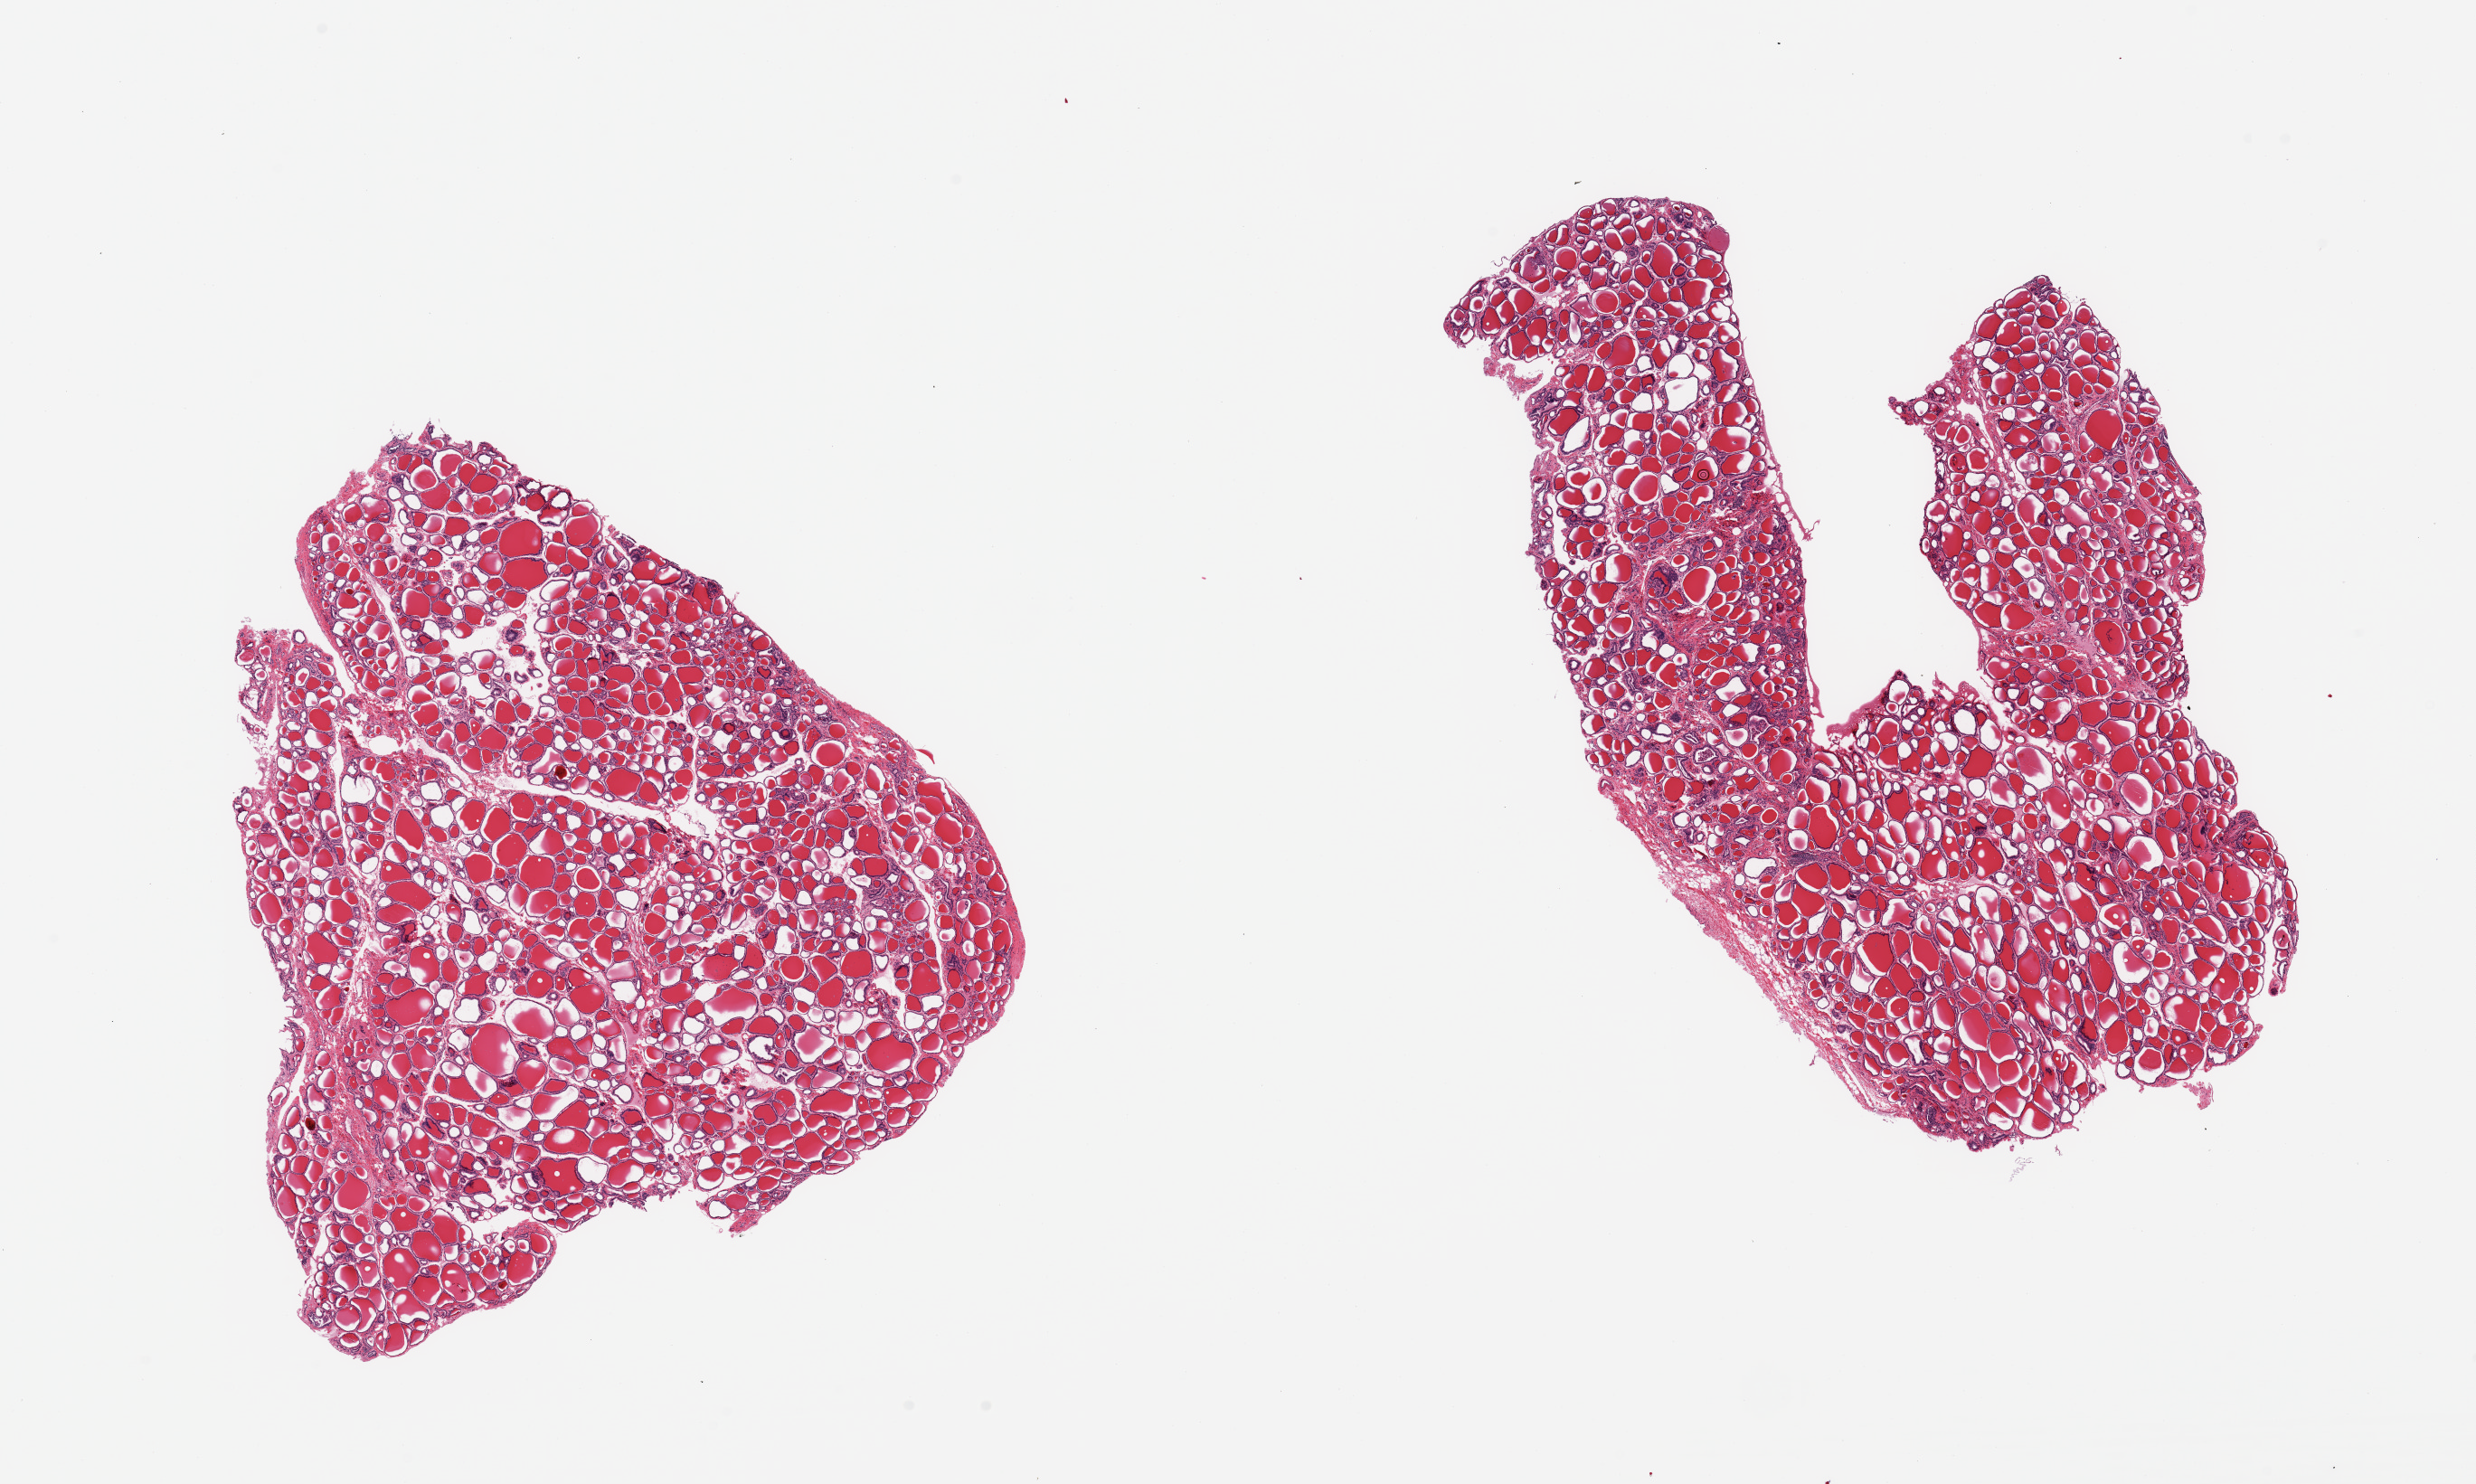
Hematoxylin and eosin (H&E) whole-slide image, low-resolution overview of the scanned area, about 21.7 x 13.0 mm (from a 20x scan). PAXgene-fixed, paraffin-embedded tissue. Target tissue: thyroid. Donor tissue sample. Donor sex: female.
Pathologist's review note for this sample: 2 pieces, no abnormalities.